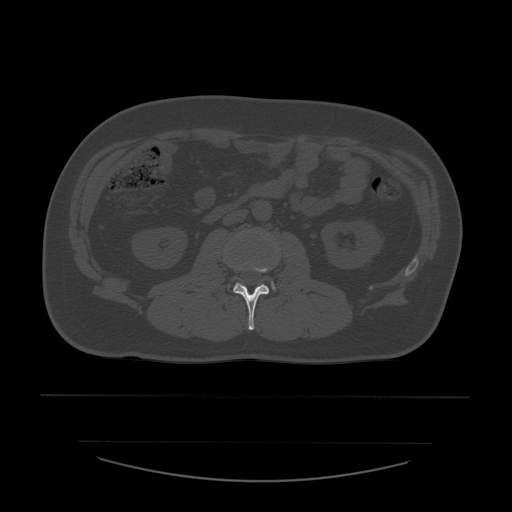
CT including the spine, one axial slice. Slice 190 of 532 in the series (ordered by position). Reconstruction kernel STANDARD. 120 kVp. Bone window (W 1800 / L 400 HU). 1.25 mm slice thickness. 512 × 512 image matrix, field of view 441 × 441 mm. Patient age 44 years. Case-level facts recorded for this patient, not image findings: primary cancer: soft tissue sarcoma.
Outlined on this slice (semi-automatic segmentation, software-assisted and operator-edited):
- L2 vertebra: bounding box <233,264,269,331> (left, top, right, bottom; pixels)
- L3 vertebra: <272,283,275,290>